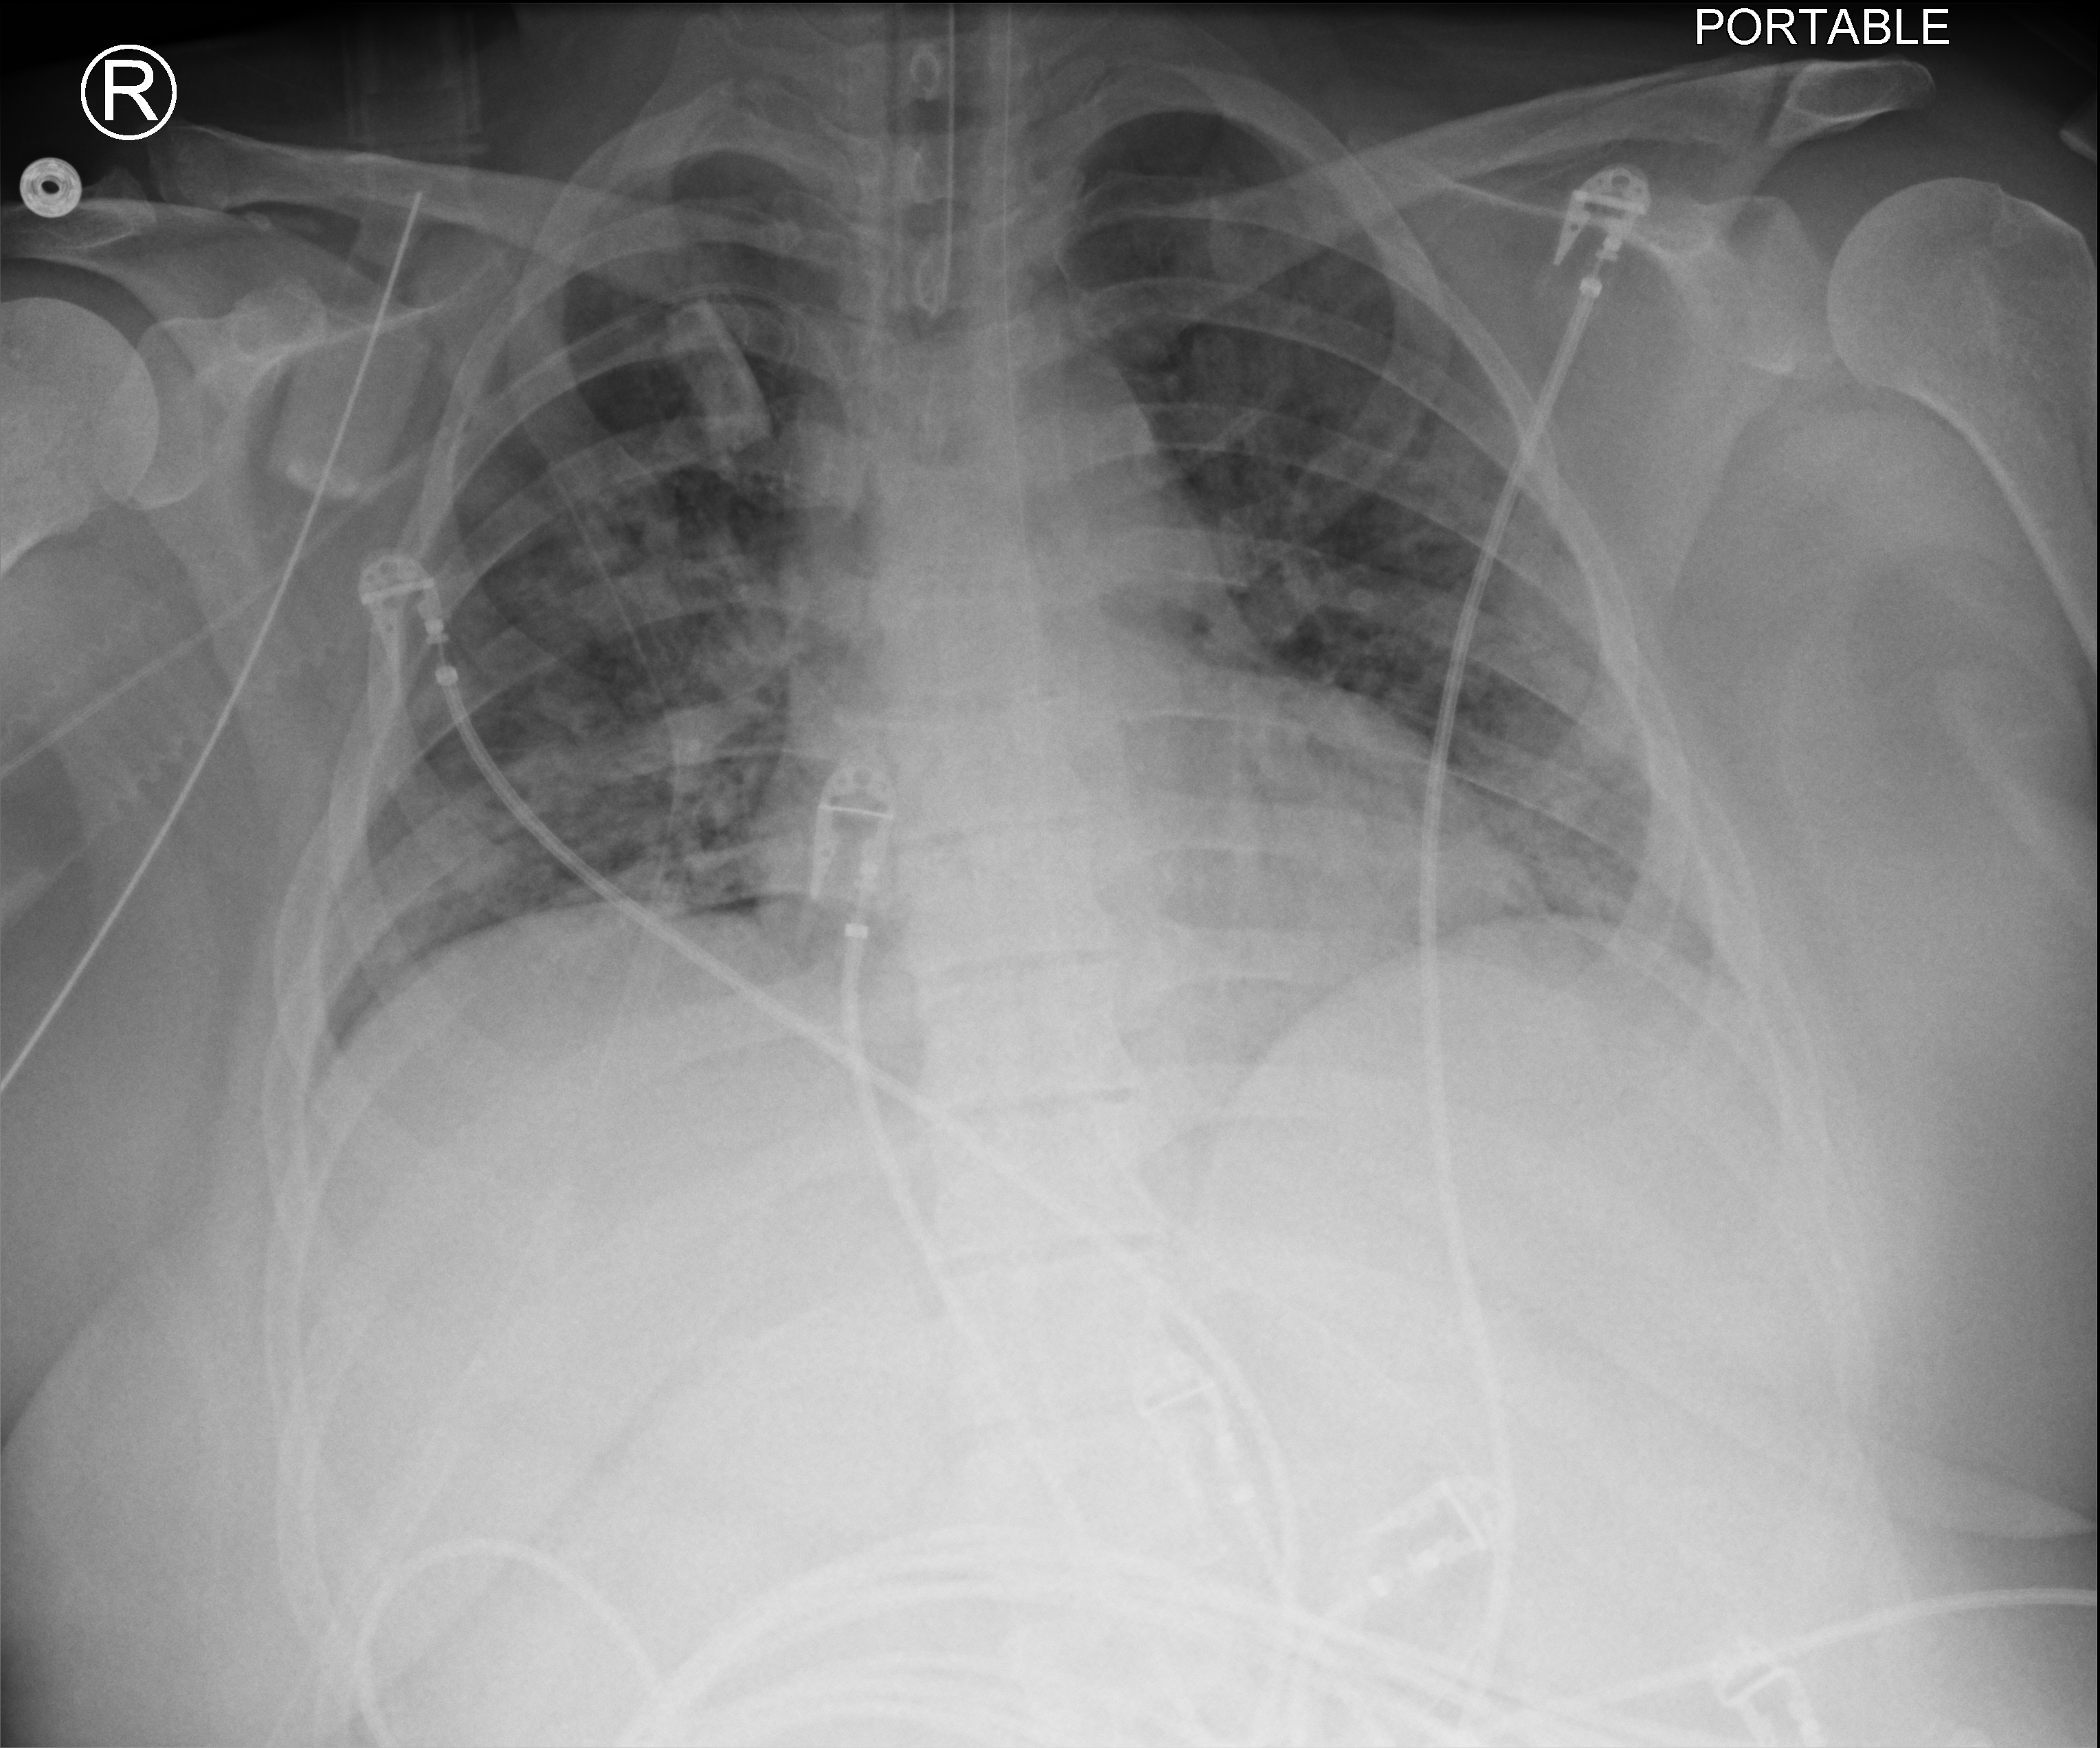
Bedside chest radiograph (computed radiography), anteroposterior (AP) projection. Female patient hospitalised with COVID-19, age 18–59 years.
Admission-level facts for this patient (not findings on this image; timing relative to this image not recorded): length of hospital stay: 25 days; admitted to intensive care during this hospital stay: yes; mechanically ventilated during this hospital stay: yes.